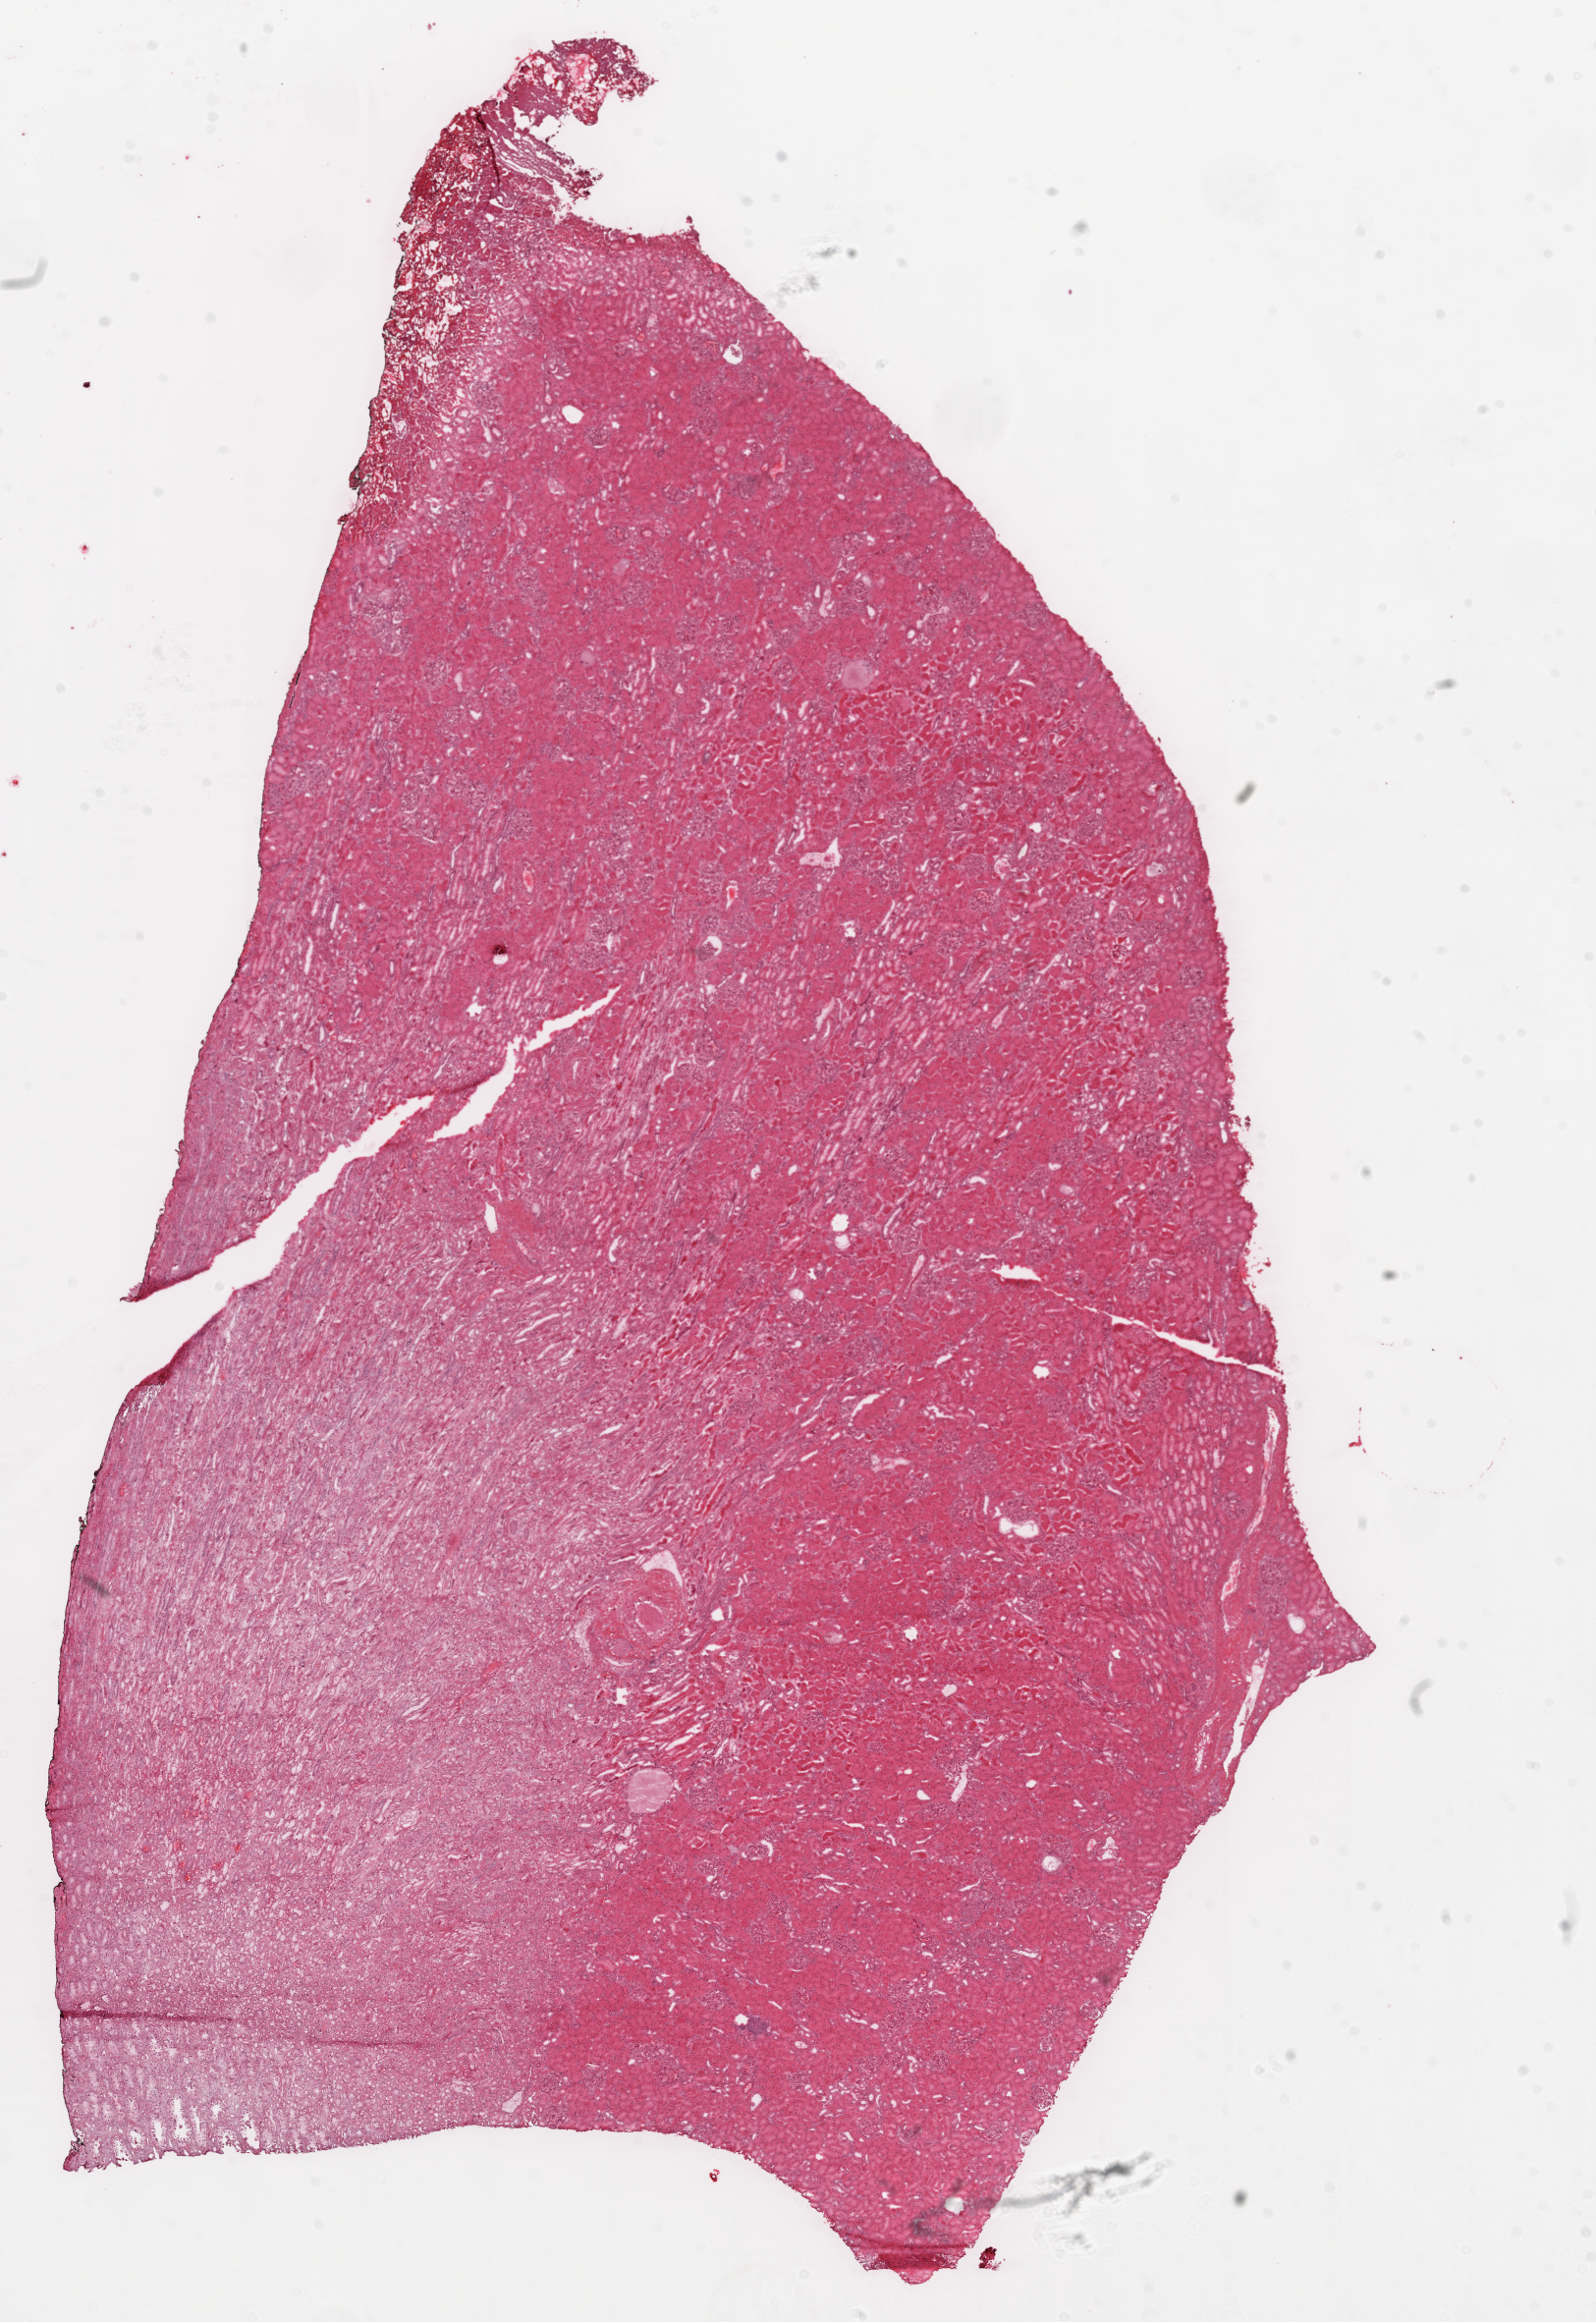
Digitized H&E-stained tissue section (whole slide), low-resolution overview of the scanned area, about 13.0 x 19.0 mm, frozen section from the top of the tissue portion, solid tissue normal (non-tumour tissue) sample from the kidney. Male patient; age at initial diagnosis 40 years.
This section: solid tissue normal sample (biorepository sample class). Patient diagnosis: Clear cell adenocarcinoma, NOS.